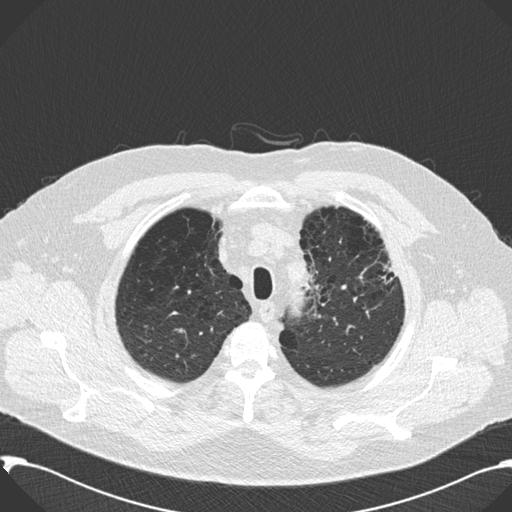
Axial slice from a low-dose chest CT screening exam. Second screening round (one year after baseline). Lung window (W 1500 / L -600 HU). 120 kVp. Slice 30 of 199 in the series. 512 × 512 image matrix. Male, age 59 years at enrolment.
Lesion marked by an expert reader, box from (x=367, y=249) to (x=408, y=307) px. Screening reader's record for this exam: no non-calcified nodule ≥4 mm recorded. Official screen result: negative screen, significant abnormalities not suspicious for lung cancer. Later outcome: lung cancer diagnosed 518 days after this screen — bronchiolo-alveolar carcinoma, mixed mucinous and non-mucinous, left upper lobe, stage IA (AJCC 6th edition), 20 mm at pathology.